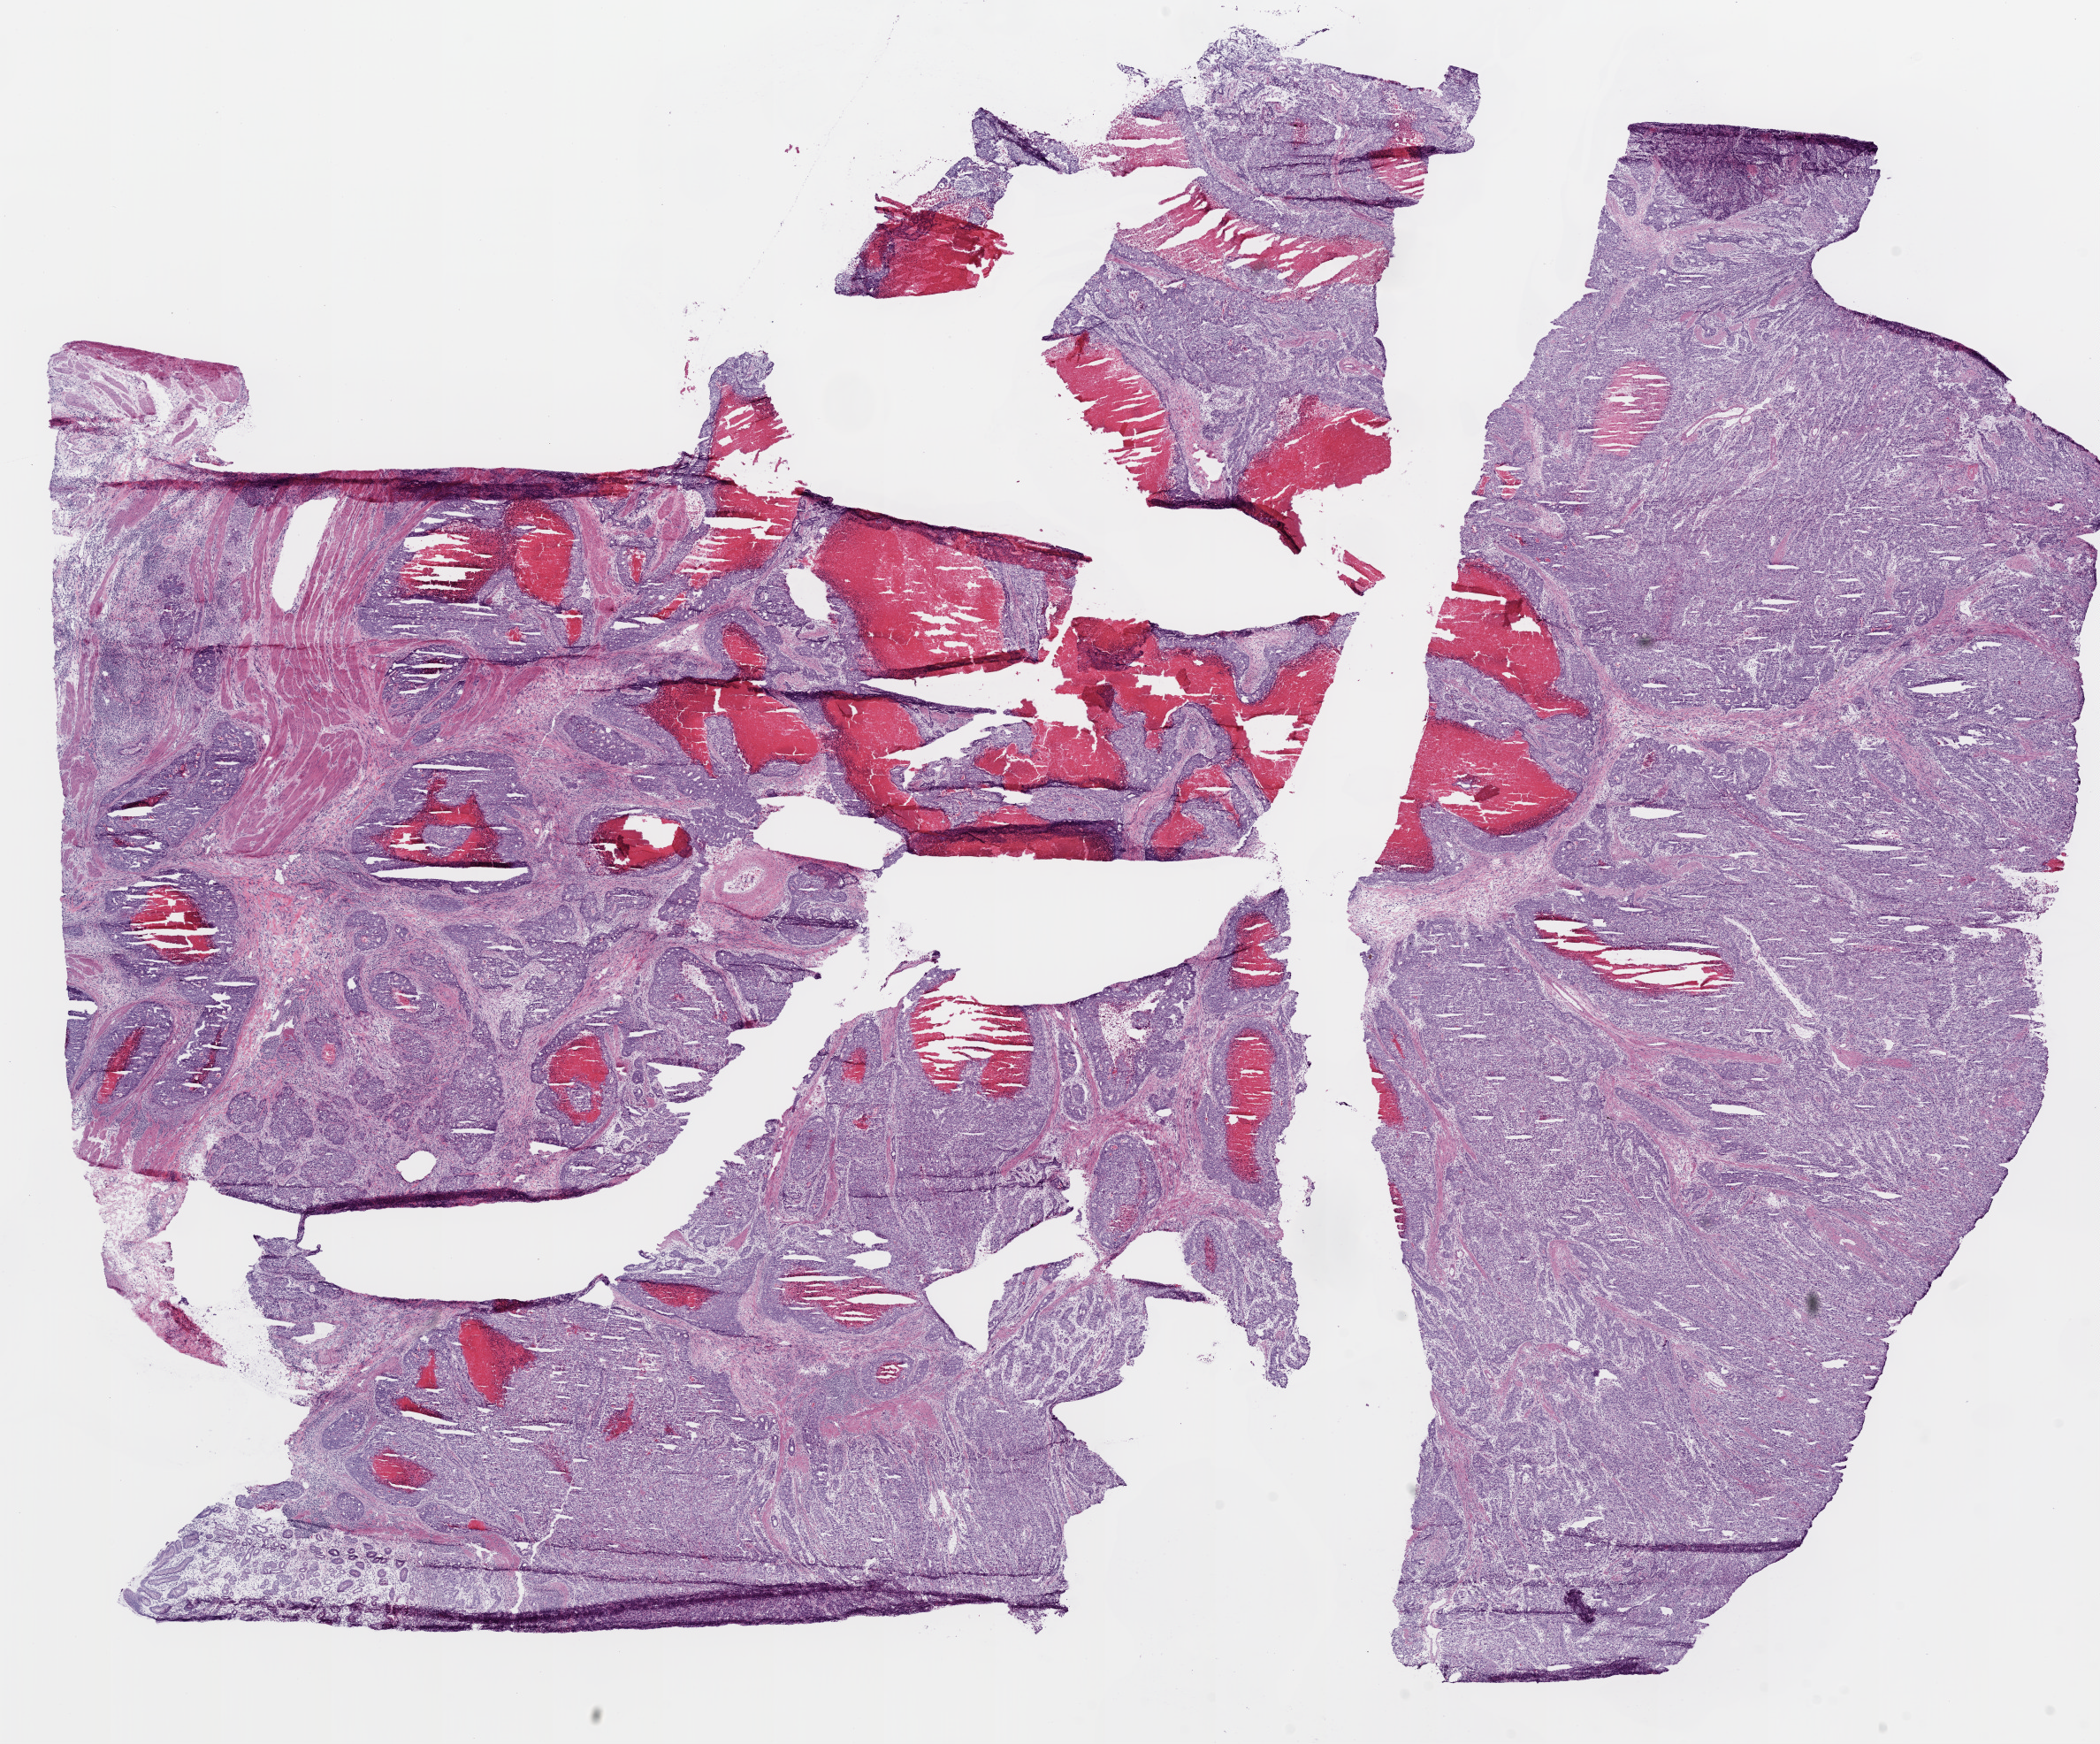
Digitized H&E-stained tissue section (whole slide) — low-resolution overview of the scanned area, about 19.1 x 15.8 mm (slide scanned at 20x), frozen section from the top of the tissue portion, sample: primary tumour, stomach. Male, age 75 years at initial diagnosis. Histologic grade: G3 (poorly differentiated). Slide review estimates, as recorded: tumour cells 75%, tumour nuclei 75%, normal cells 5%, stromal cells 5%, necrosis 15%.
- diagnosis: Adenocarcinoma, NOS (cardia, NOS)